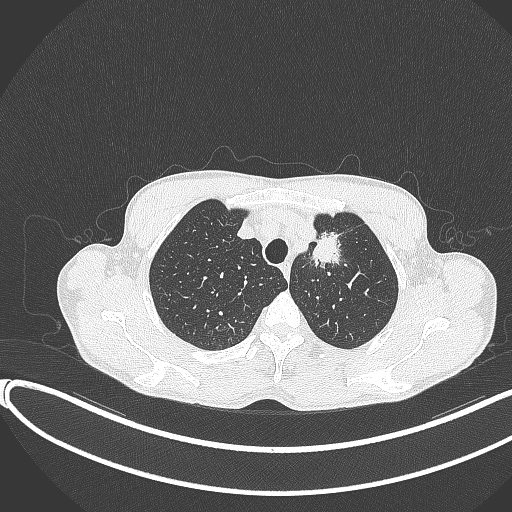
Chest CT, one axial slice; lung window (W 1500 / L -600 HU); 512 × 512 image matrix, field of view 400 × 400 mm. Male patient, age 58 years. Case-level facts recorded for this patient, not image findings: clinical TNM (as recorded): T1c N1 M0.
Outlined on this slice (rectangle marked by the reading radiologist):
- lung tumour (recorded histology: adenocarcinoma): bounding box (x1, y1, x2, y2) in pixels: (299, 223, 349, 280)